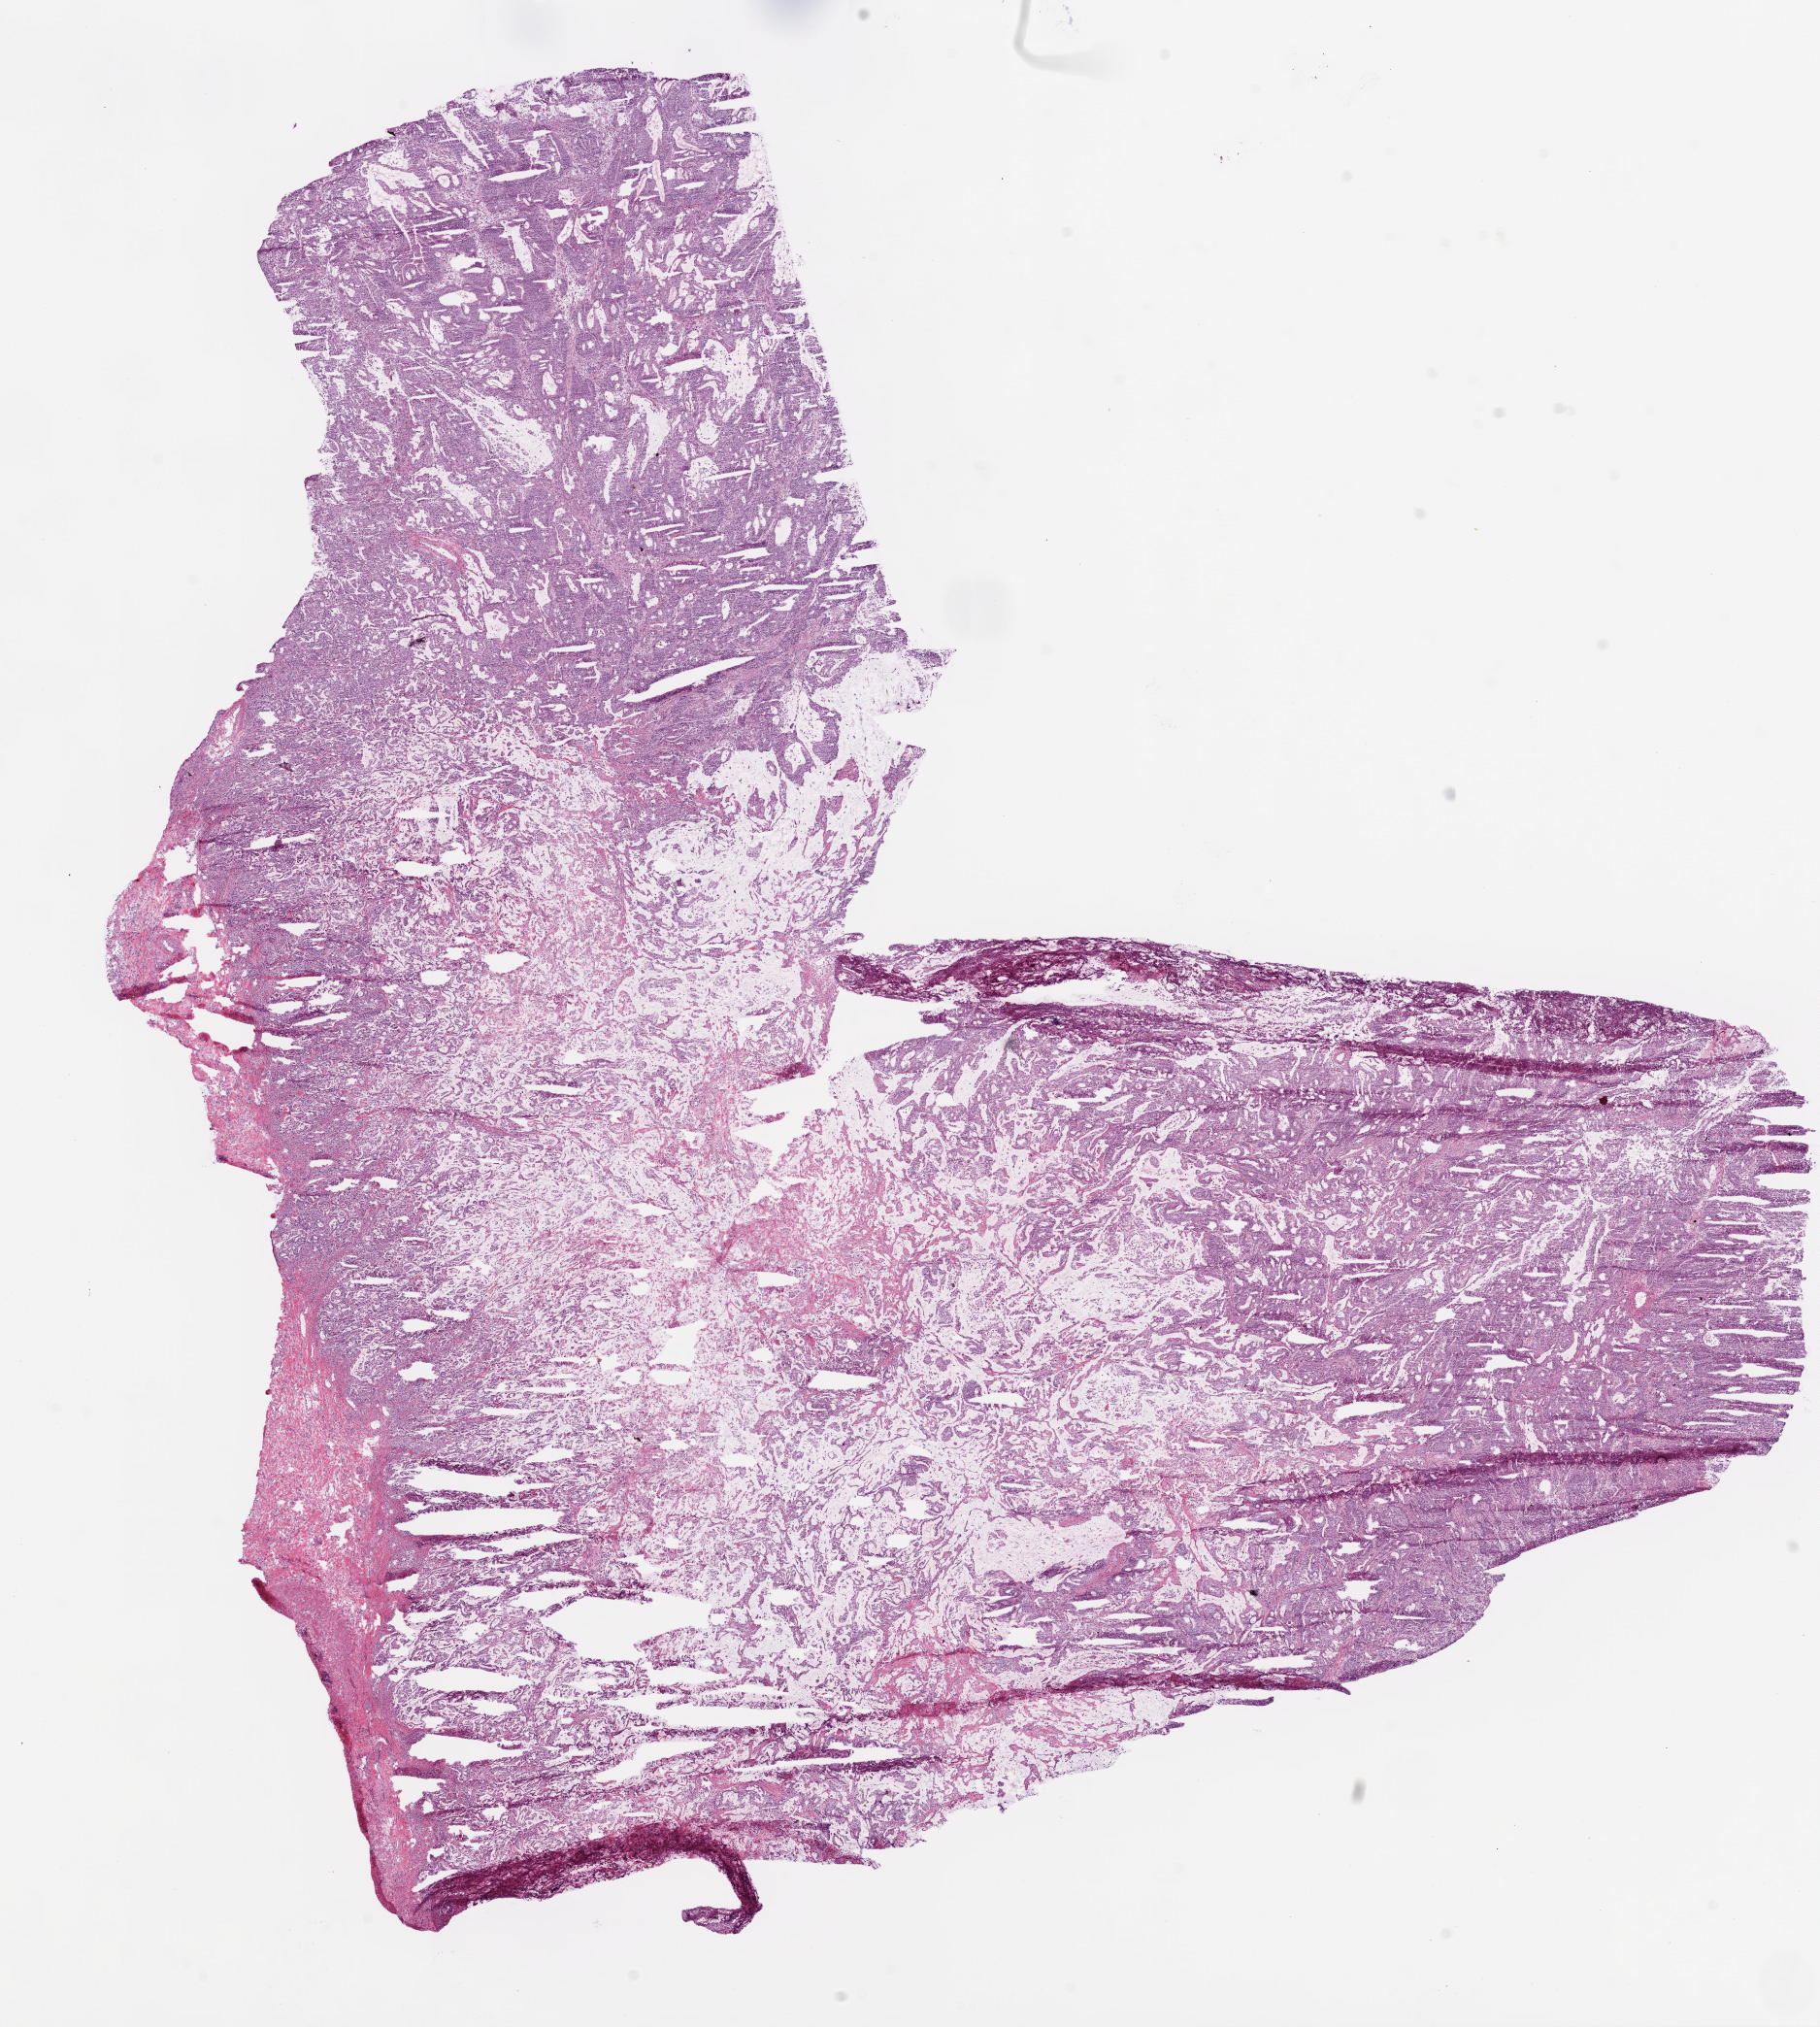
Digitized Hematoxylin and eosin (H&E) stained tissue section (whole slide), a low-resolution overview of the entire scanned area, about 15.0 x 16.8 mm (from a 20x scan), frozen section, primary tumour sample from the stomach. Female, age 79 years at initial diagnosis. Histologic grade: G2 (moderately differentiated). Slide review estimates, as recorded: tumour cells 82%, tumour nuclei 85%, normal cells 5%, stromal cells 10%, necrosis 3%.
Histologic diagnosis: Adenocarcinoma, NOS (gastric antrum).